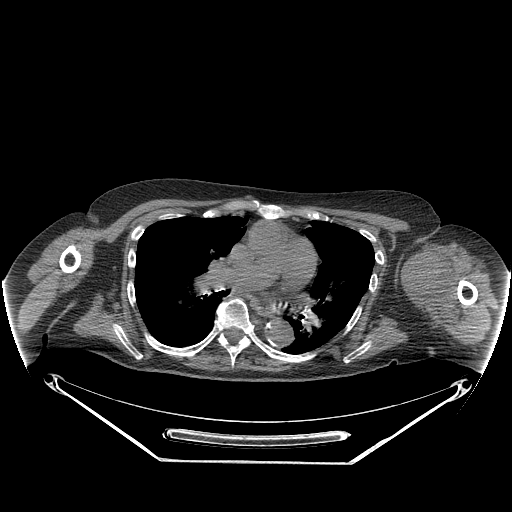
CT of an extremity soft-tissue mass (from a PET/CT study), one axial slice; reconstruction kernel STANDARD; 140 kVp; soft-tissue window (W 400 / L 40 HU); 3.75 mm slice thickness; 512 × 512 image matrix. Female patient. From the clinical record (not read from this slice): histological type: pleiomorphic leiomyosarcoma; grade: high; site of the primary tumour: left biceps.
Annotated regions visible in this slice (expert contour drawn on MRI and transferred to this co-registered scan by the dataset authors):
- gross tumour volume including surrounding oedema: bounding box <409,247,458,321> (left, top, right, bottom; pixels)
- gross tumour volume (mass): <407,247,457,305>